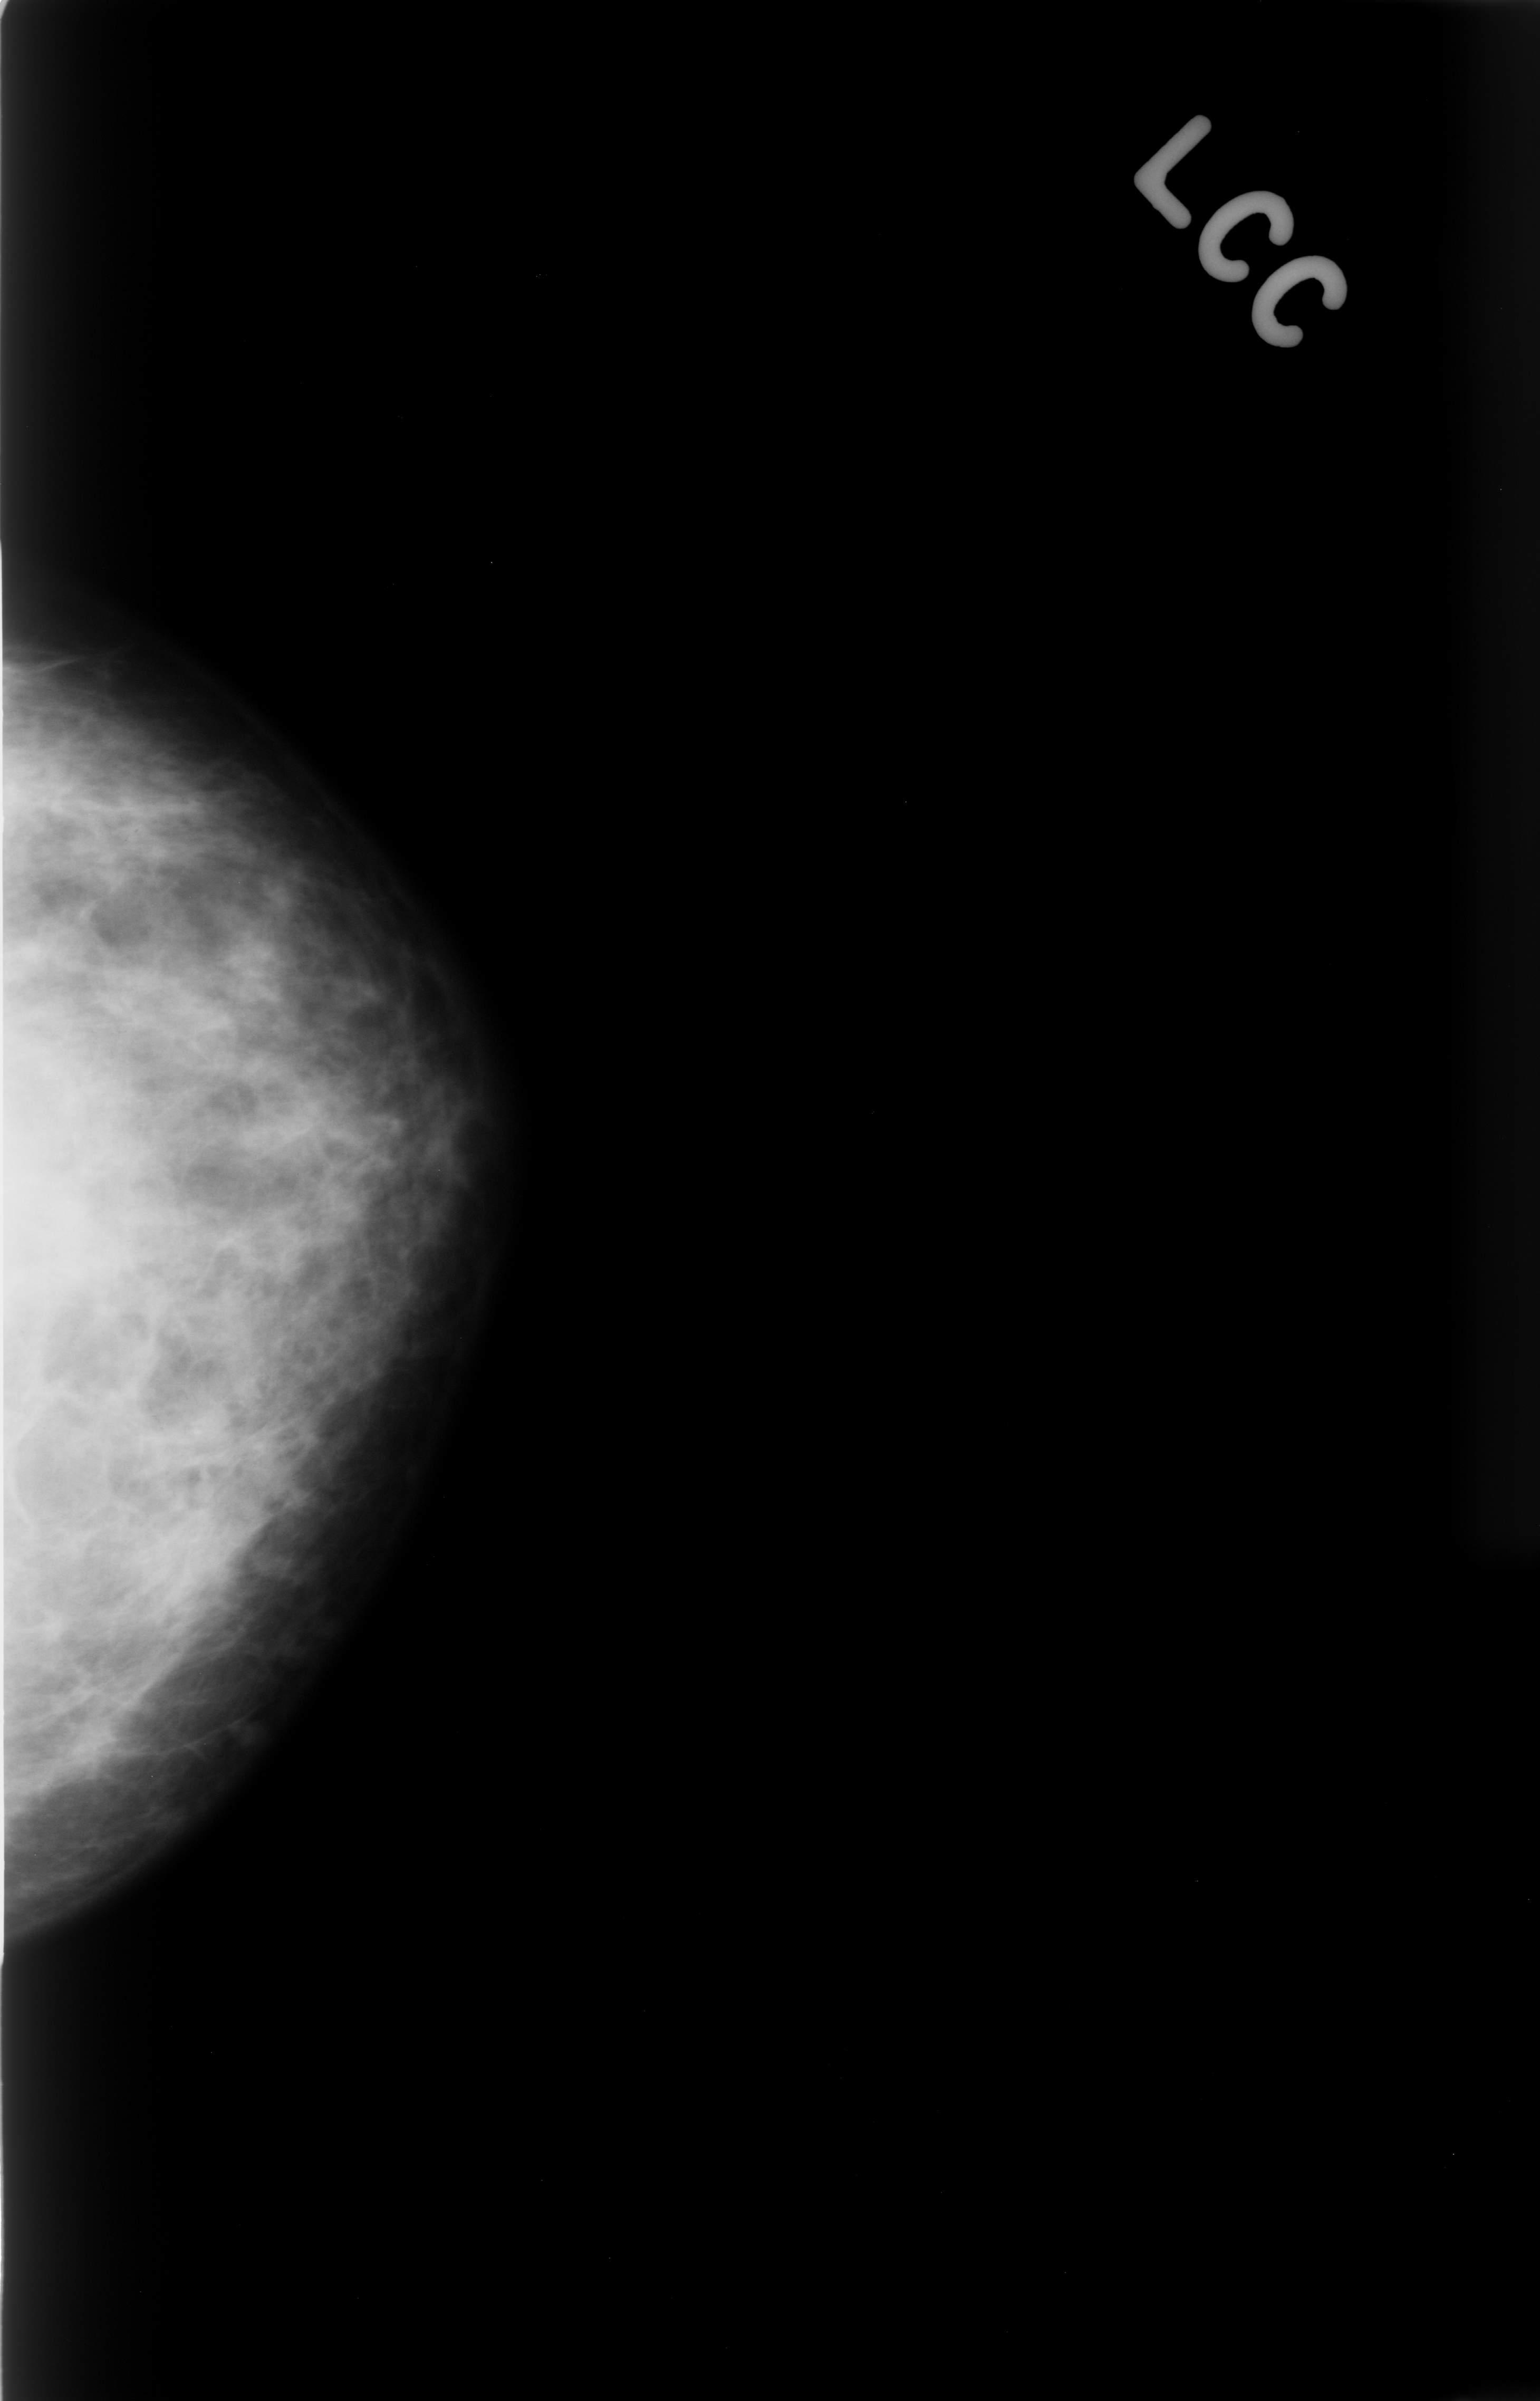
Mammogram (digitized film); left breast; craniocaudal (CC) view; breast composition: heterogeneously dense (BI-RADS density category 3 of 4); 1540 × 2401 image matrix.
Expert-marked regions of interest on this film, with their recorded descriptors:
- mass, shape asymmetric breast tissue, margins ill defined; BI-RADS assessment category 5; subtlety rating 2 on a 1 (subtle) to 5 (obvious) scale; pathology (as recorded): malignant: bounding box <0,1049,157,1372> (left, top, right, bottom; pixels)